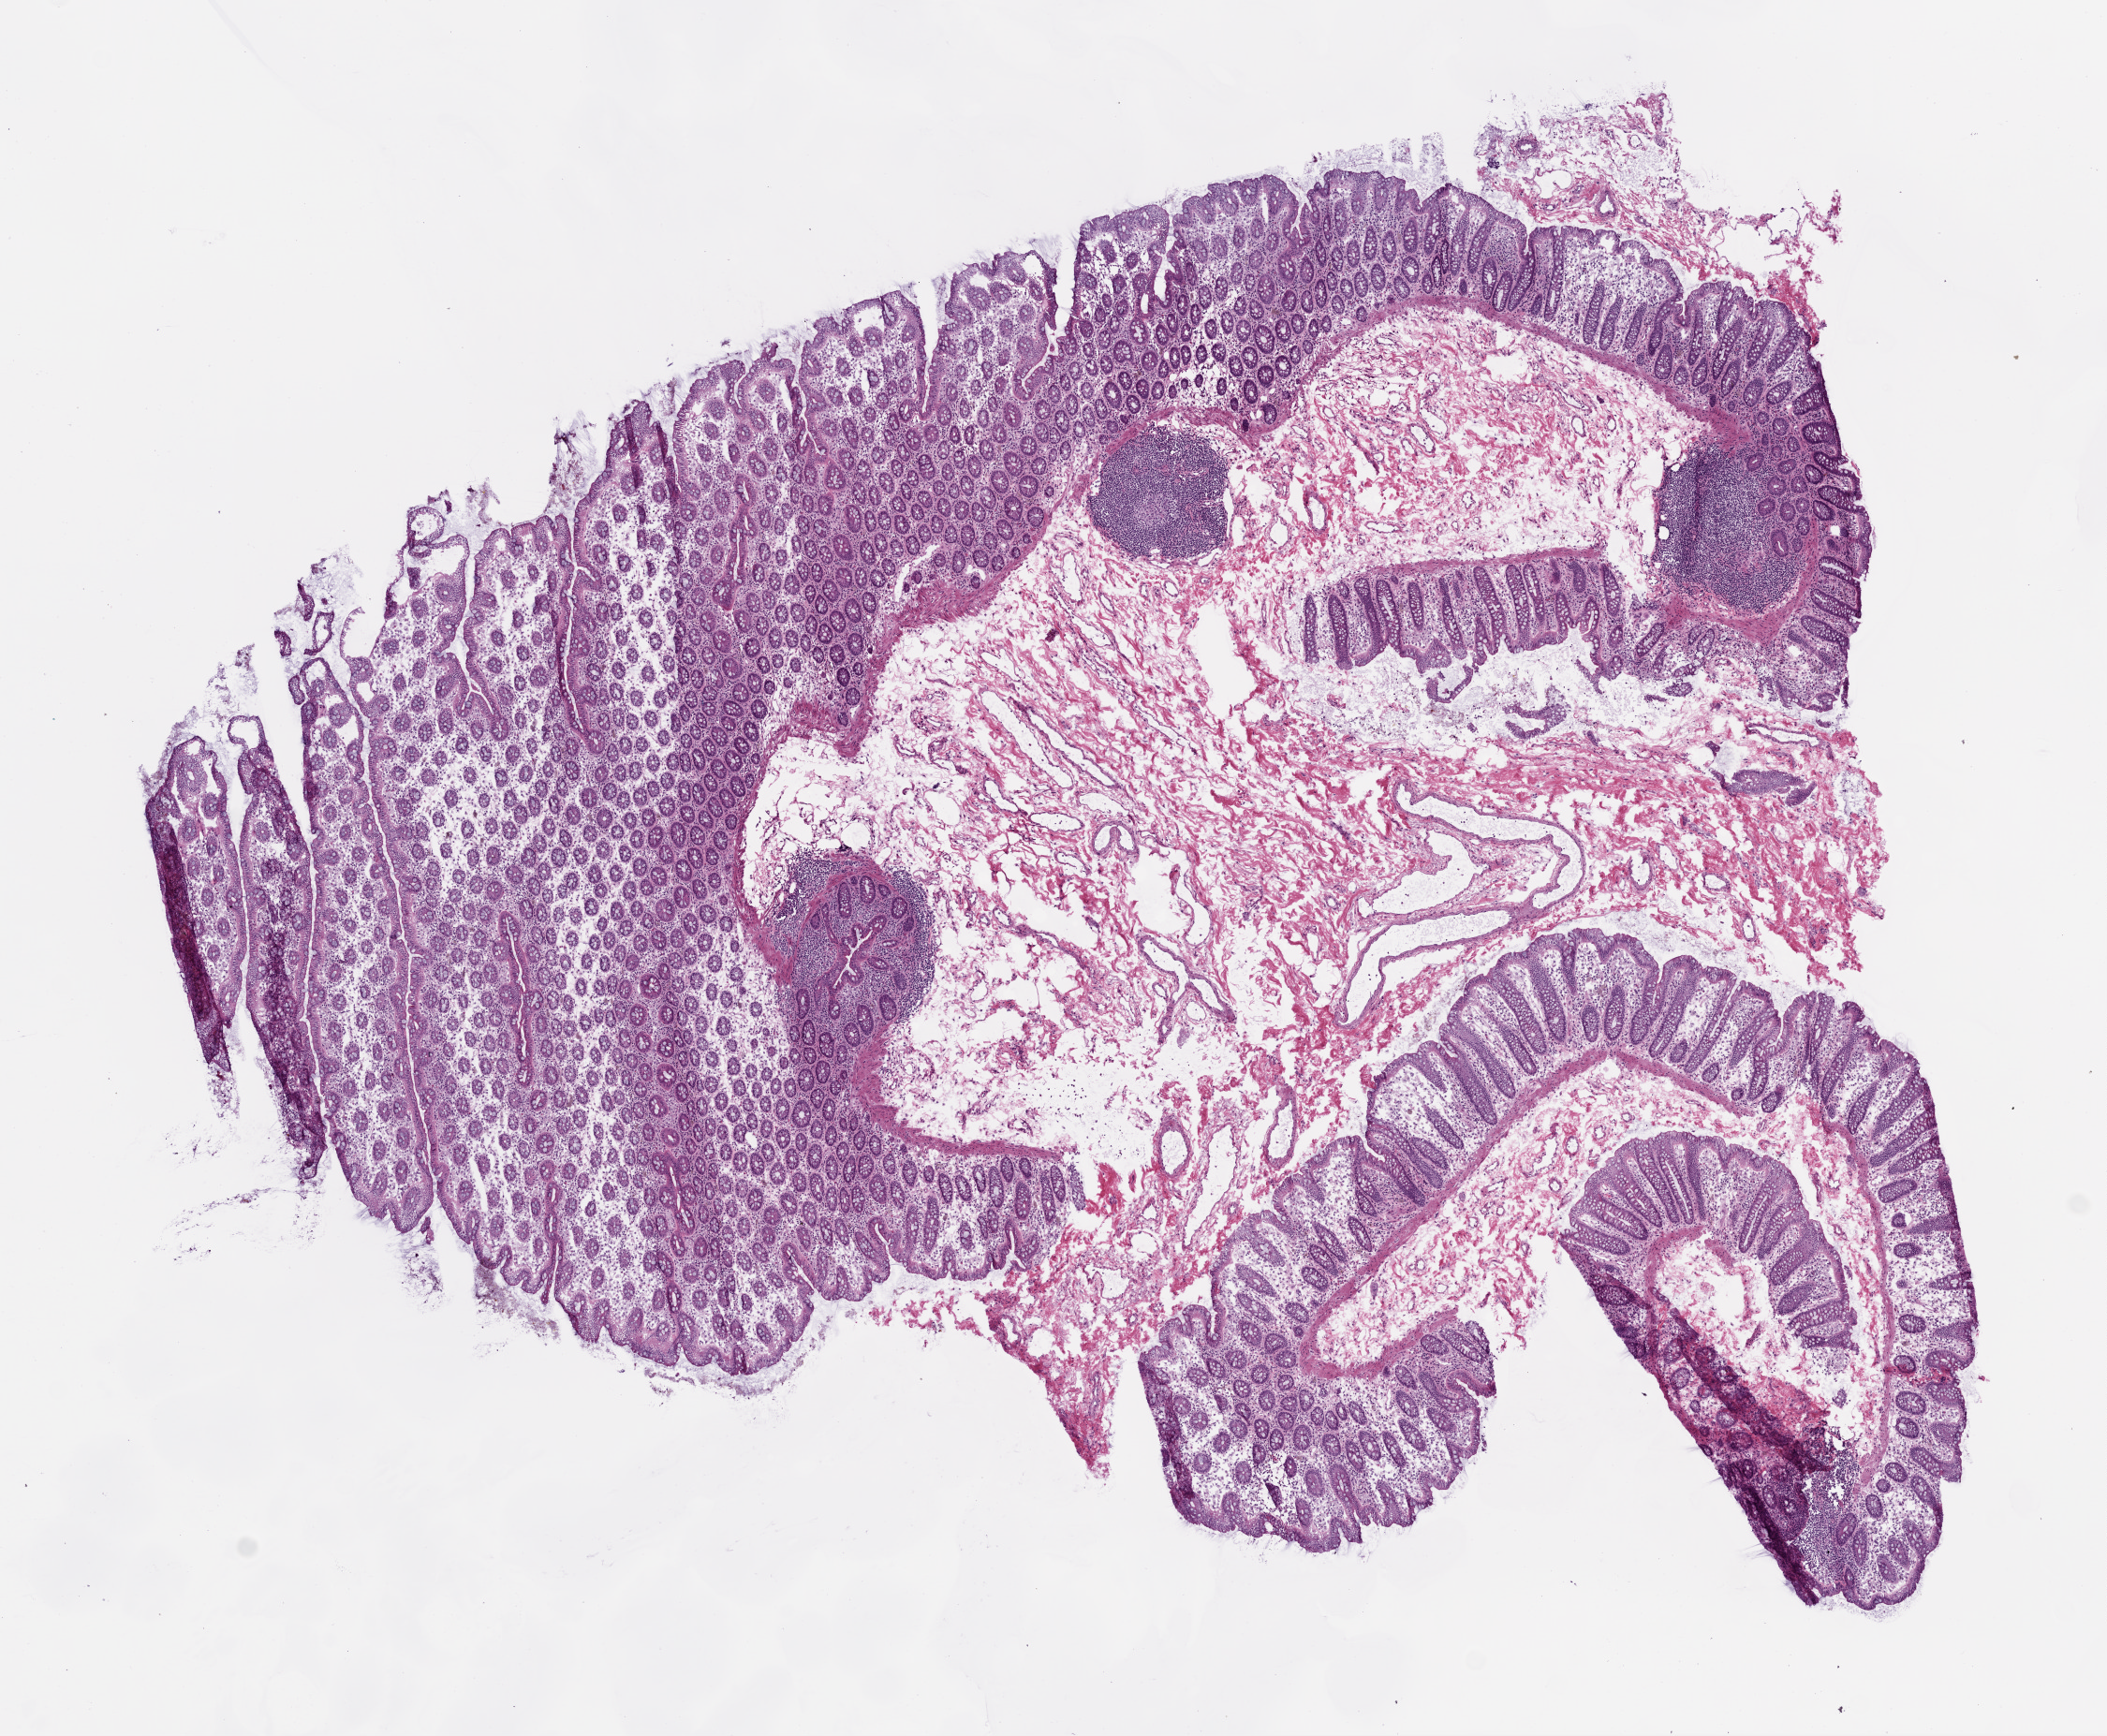
Digitized Hematoxylin and eosin (H&E) stained tissue section (whole slide) — a low-resolution overview of the entire scanned area, about 9.0 x 7.4 mm (acquisition: 20x scan). Frozen section from the top of the tissue portion. Sample: solid tissue normal (non-tumour tissue), colon. Female, age 84 years at initial diagnosis.
This section: solid tissue normal sample (biorepository sample class). Patient diagnosis: Adenocarcinoma, NOS.